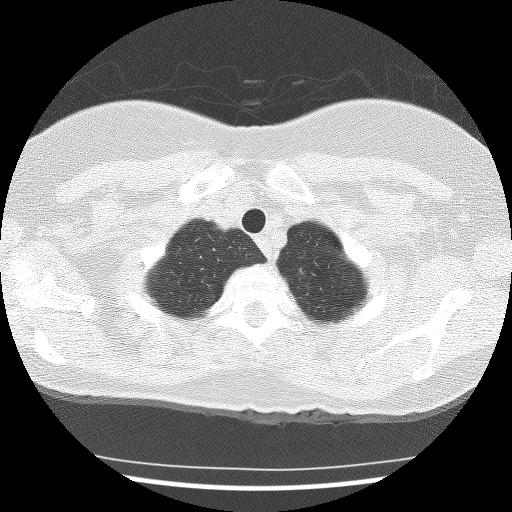
Chest CT (low-dose screening protocol), one axial image; first (baseline) screen; lung window (W 1500 / L -600 HU); 2.5 mm slice thickness; lung (sharp) reconstruction kernel (BONE); 120 kVp; slice 11 of 120 in the series; 512 × 512 image matrix. Female, age 59 years at enrolment.
Expert-annotated lung lesion, bounding box [x1, y1, x2, y2] px = [281, 257, 321, 296]. The screening reader recorded 3 non-calcified nodules or masses ≥4 mm on this exam (left upper lobe, right upper lobe, right upper lobe); which of them this box marks is not recorded. Official screen result: positive, change unspecified: nodule(s) >= 4 mm or enlarging nodule(s), mass(es), or other non-specific abnormalities suspicious for lung cancer. Later outcome: lung cancer diagnosed 867 days after this screen — bronchiolo-alveolar adenocarcinoma, NOS, left upper lobe, well differentiated (G1), stage IA (AJCC 6th edition), 10 mm at pathology.